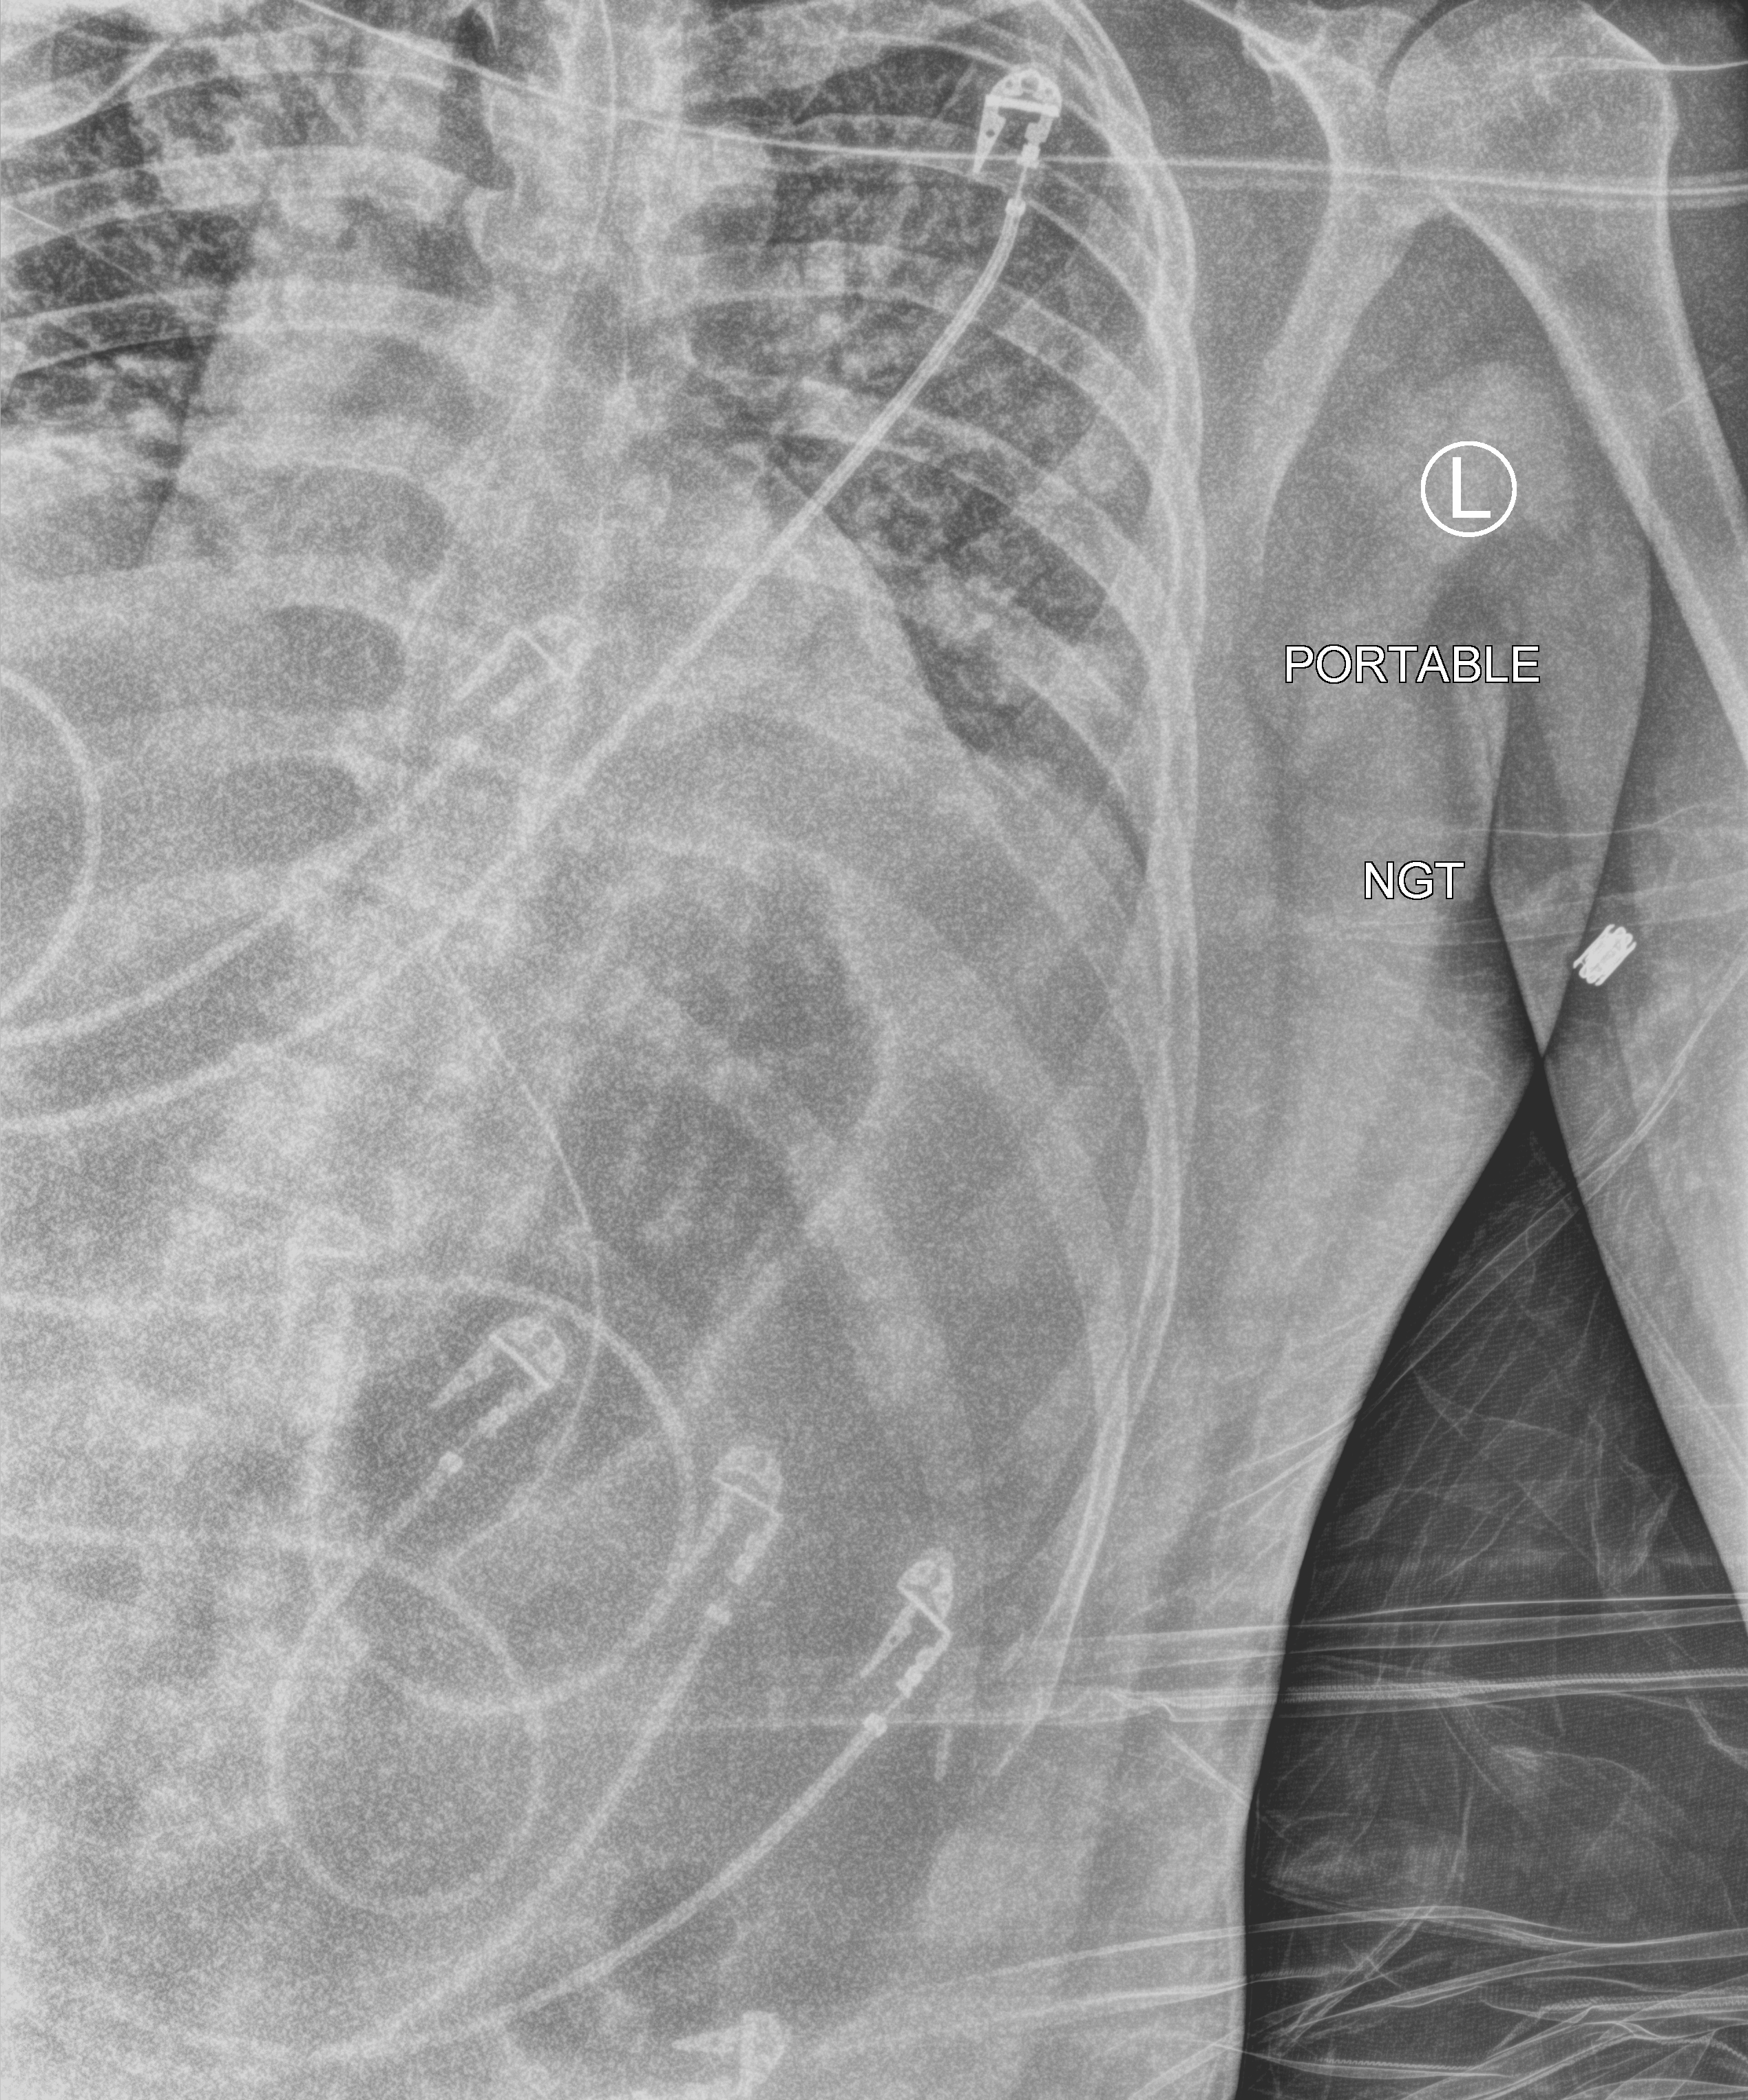
Chest X-ray (portable); anteroposterior (AP) projection. Male patient hospitalised with COVID-19, age 18–59 years.
From the hospital-stay record, not from the radiograph (when in the stay this image was taken is not recorded): other chronic lung disease (admission record): no; mechanically ventilated during this hospital stay: yes; admitted to intensive care during this hospital stay: yes.